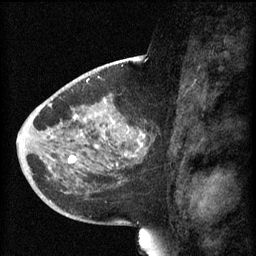
Breast MRI (dynamic contrast-enhanced), one sagittal slice. Slice 29 of 60 in the series (ordered by position). 3 images stored at this slice position (order not interpretable as contrast timing). 1.5 T. TE 4.2 ms, TR 8.1 ms. 256 × 256 image matrix. Female patient, age 44 years.
Annotated regions visible in this slice (semi-automatically segmented with operator editing):
- analysis volume of interest (the breast-tissue region the enhancement analysis was run in; not a lesion): box from (x=59, y=110) to (x=151, y=169) px
- tumour enhancement mask (voxels above the 70 % enhancement threshold inside the analysis volume of interest): (x=68, y=118)–(x=145, y=169)